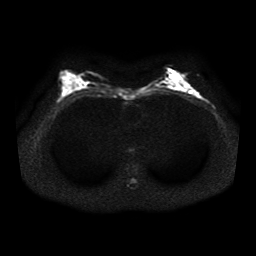
Breast MRI, one axial slice. Slice 21 of 41 in the series (ordered by position). Diffusion-weighted series; image 2 of 4 stored at this slice position (different b-values; order by instance number). 1.5 T. 256 × 256 image matrix, field of view 330 × 330 mm. Female patient.
Structures marked on this image (outlined manually by an expert reader):
- tumour on diffusion-weighted imaging: bounding box (x1, y1, x2, y2) in pixels: (194, 92, 198, 96)